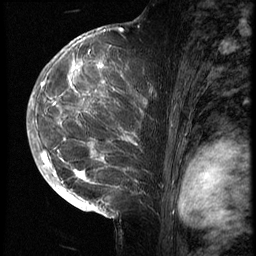
Breast MRI (dynamic contrast-enhanced), one sagittal slice; position 40 of 70 along the scan axis; 3 images stored at this slice position (order not interpretable as contrast timing); 1.5 T; TE 4.2 ms, TR 9 ms; 256 × 256 image matrix, field of view 180 × 180 mm. Patient: female, 28 years. From the clinical record (not read from this slice): setting: breast cancer imaged before/during neoadjuvant chemotherapy.
Structures marked on this image (semi-automatically segmented with operator editing):
- analysis volume of interest (the breast-tissue region the enhancement analysis was run in; not a lesion): box from (x=43, y=42) to (x=161, y=215) px
- tumour enhancement mask (voxels above the 140 % enhancement threshold inside the analysis volume of interest): (x=43, y=46)–(x=136, y=207)